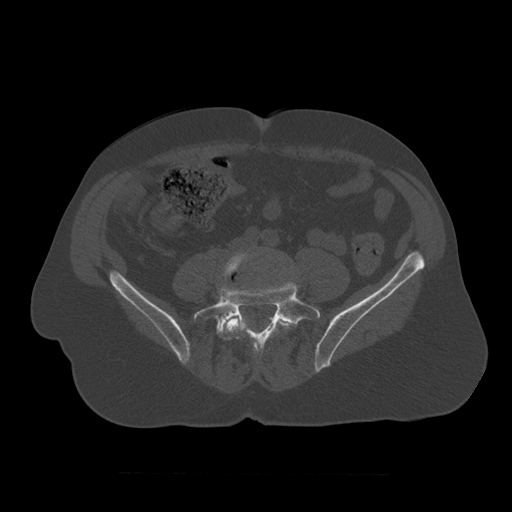
CT including the spine, one axial slice; position 262 of 450 along the scan axis; reconstruction kernel STANDARD; 120 kVp; bone window (W 1800 / L 400 HU); 1.25 mm slice thickness; 512 × 512 image matrix, field of view 405 × 405 mm. Patient age 75 years. Case-level facts recorded for this patient, not image findings: primary cancer: prostate.
Structures marked on this image (semi-automatically segmented with operator editing):
- L4 vertebra: bounding box [x1, y1, x2, y2] px = [223, 252, 293, 354]
- L5 vertebra: [194, 279, 321, 352]